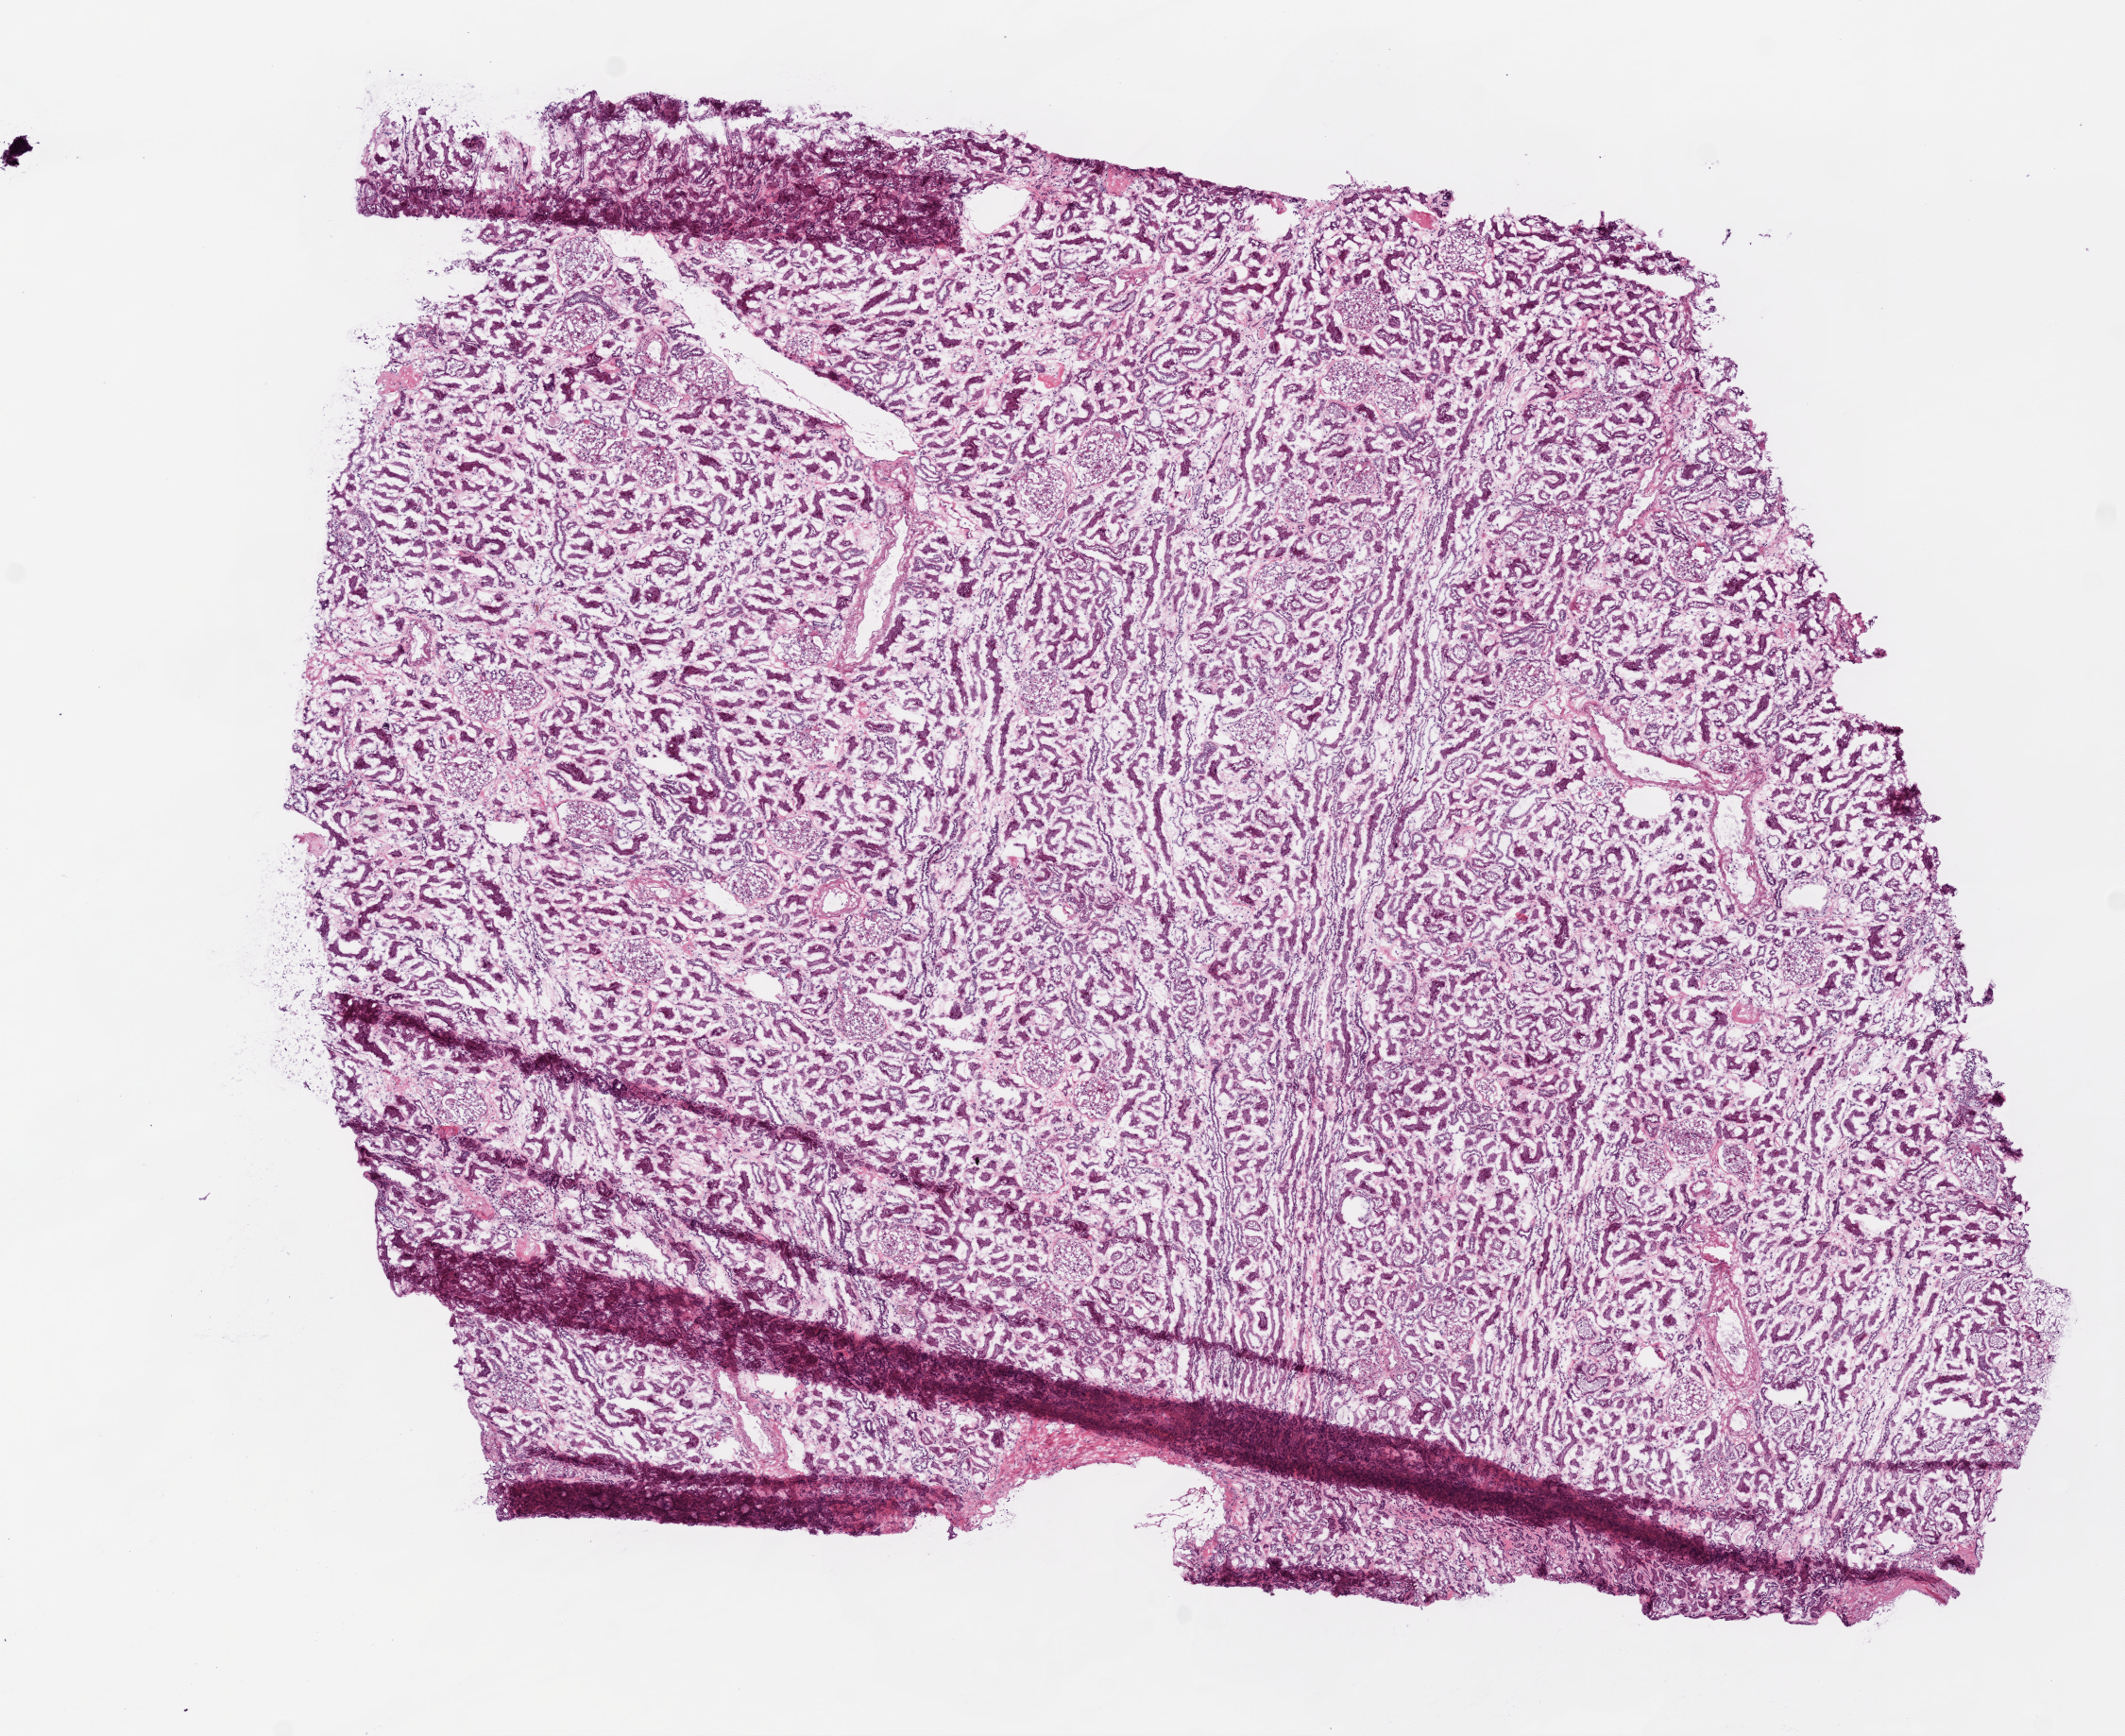
Hematoxylin and eosin (H&E) stained whole-slide image, whole scanned area (about 9.0 x 7.4 mm, slide scanned at 20x) shown as a low-resolution overview; frozen section; kidney, solid tissue normal (non-tumour tissue) sample. Patient sex: female.
• this section: solid tissue normal (non-tumour) sample from the same patient
• patient diagnosis: Clear cell adenocarcinoma, NOS